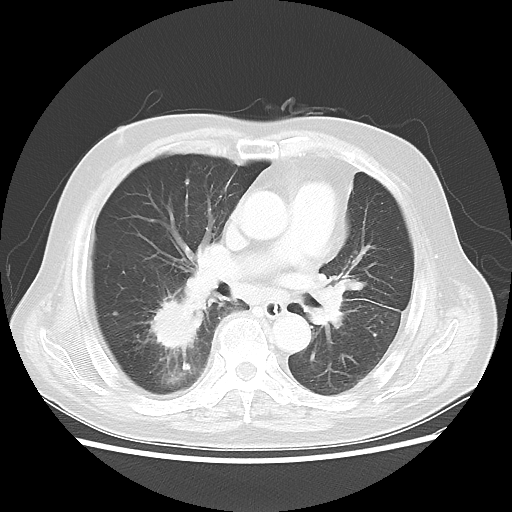
Chest CT, one axial slice; reconstruction kernel LUNG; lung window (W 1500 / L -600 HU); 5 mm slice thickness; 512 × 512 image matrix. Patient: male, 83 years. From the clinical record (not read from this slice): clinical TNM (as recorded): T2 N3 M0.
Outlined on this slice (bounding box drawn by a radiologist):
- lung tumour (recorded histology: adenocarcinoma): bounding box (x1, y1, x2, y2) in pixels: (149, 291, 206, 356)